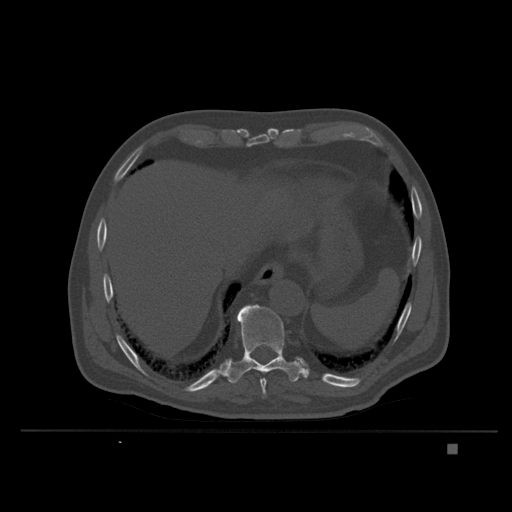
CT including the spine, one axial slice; slice 197 of 435 in the series (ordered by position); bone window (W 1800 / L 400 HU); 1.5 mm slice thickness; 512 × 512 image matrix. Patient: male, 73 years. Case-level facts recorded for this patient, not image findings: primary cancer: skin.
Outlined on this slice (semi-automatically segmented with operator editing):
- T10 vertebra: bounding box (x1, y1, x2, y2) in pixels: (227, 304, 306, 384)
- T9 vertebra: (258, 370, 267, 398)